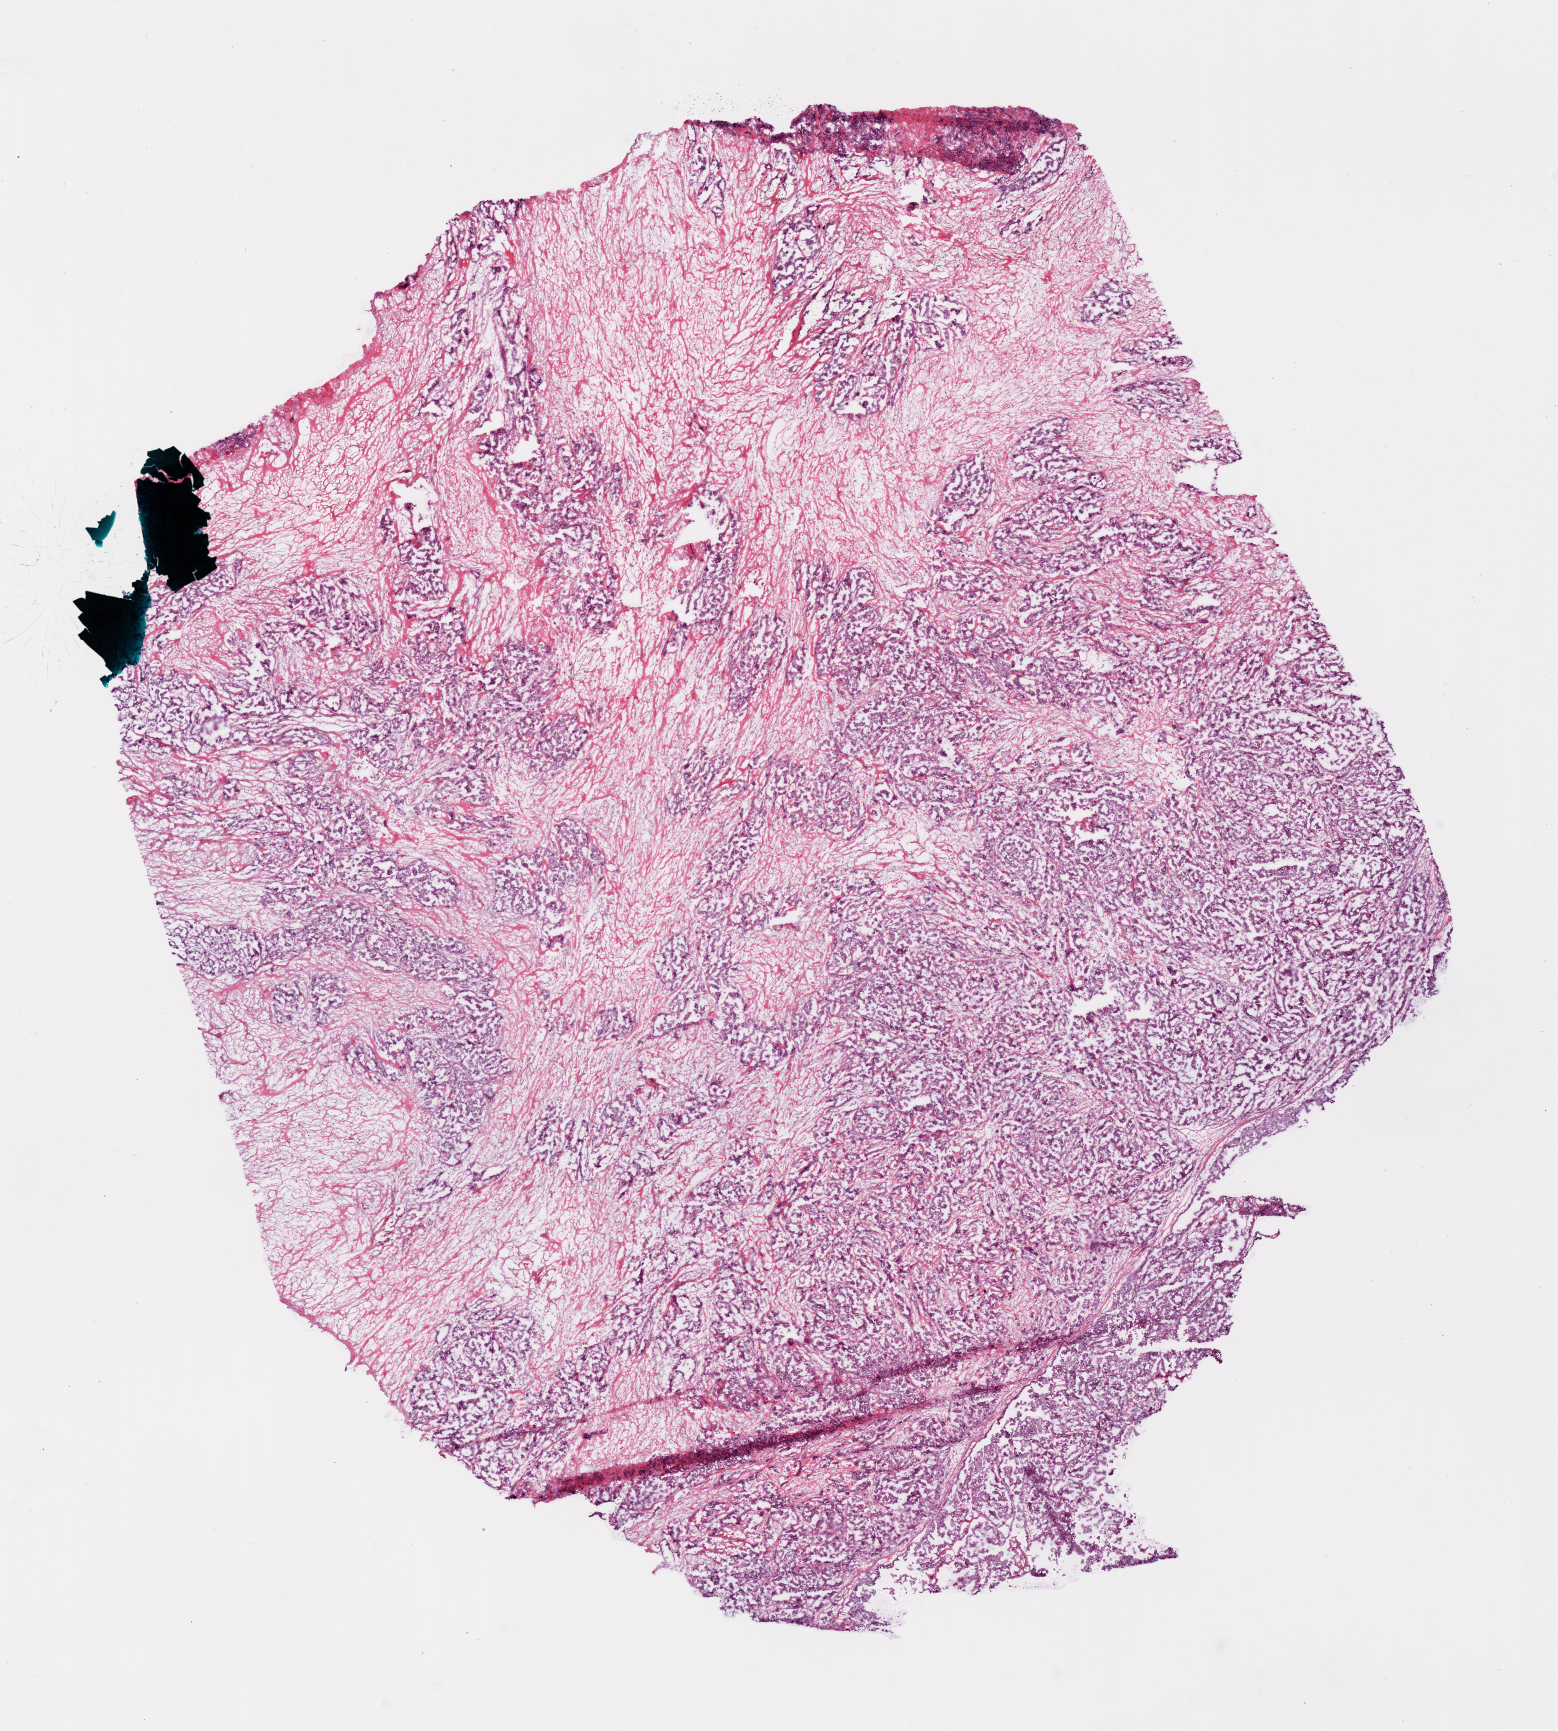
Hematoxylin and eosin (H&E) stained whole-slide image — shown as a low-resolution overview of the whole scanned area (about 12.6 x 14.0 mm, acquisition: 20x scan). Frozen section. Sample: primary tumour, ovary. Patient: female, age at initial diagnosis 36 years. Histologic grade: G3 (poorly differentiated). Composition of this section per pathologist review: tumour nuclei 90%, necrosis 5%.
Pathologic diagnosis: Serous cystadenocarcinoma, NOS. FIGO stage: IIIC. Laterality: bilateral.